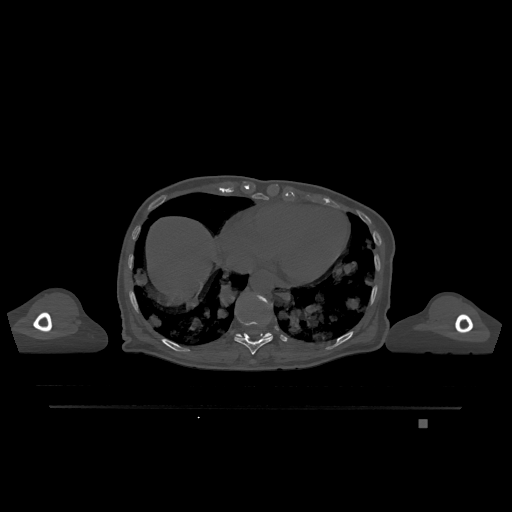
CT including the spine, one axial slice. Position 627 of 1317 along the scan axis. Bone window (W 1800 / L 400 HU). 0.5 mm slice thickness. 512 × 512 image matrix, field of view 500 × 500 mm. Patient: female, 74 years. Case-level facts recorded for this patient, not image findings: primary cancer: lung; vertebrae with lytic lesions (as recorded): T1, T4, T5, T6, L4, L5.
Annotated regions visible in this slice (semi-automatic segmentation, software-assisted and operator-edited):
- T10 vertebra: box from (x=234, y=313) to (x=273, y=355) px
- T11 vertebra: (x=236, y=295)–(x=271, y=338)